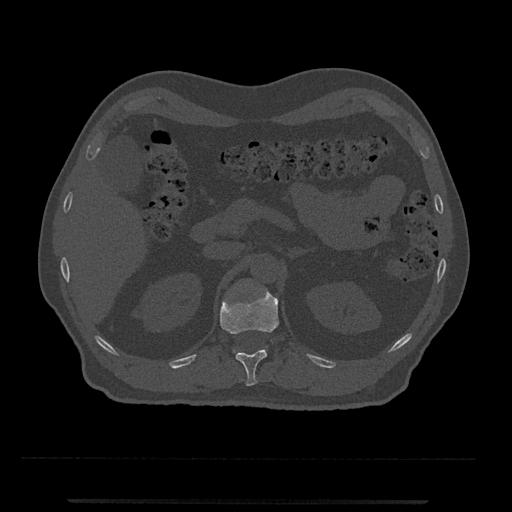
CT including the spine, one axial slice; position 382 of 797 along the scan axis; bone window (W 1800 / L 400 HU); 512 × 512 image matrix. Patient: male, 63 years. From the clinical record (not read from this slice): primary cancer: prostate.
Outlined on this slice (semi-automatically segmented with operator editing):
- T12 vertebra: bounding box <220,288,279,386> (left, top, right, bottom; pixels)